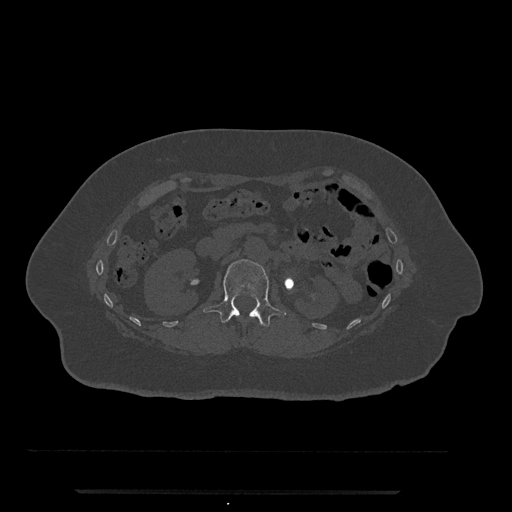
CT including the spine, one axial slice; position 109 of 797 along the scan axis; bone window (W 1800 / L 400 HU); 512 × 512 image matrix. Female patient, age 51 years. Case-level facts recorded for this patient, not image findings: primary cancer: neuro; vertebrae with lytic lesions (as recorded): T8.
Structures marked on this image (semi-automatic segmentation, software-assisted and operator-edited):
- L1 vertebra: bounding box [x1, y1, x2, y2] px = [203, 259, 287, 327]